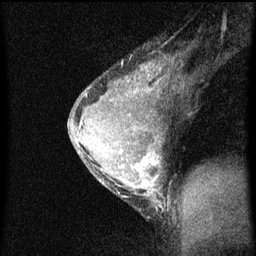
Breast MRI (dynamic contrast-enhanced), one sagittal slice. Slice 42 of 60 in the series (ordered by position). Dynamic contrast-enhanced series, image 2 of 3 at this slice position (ordered by acquisition). 1.5 T. TE 4.2 ms, TR 8 ms. 2 mm slice thickness. 256 × 256 image matrix, field of view 180 × 180 mm. Patient: female, 33 years.
Outlined on this slice (semi-automatic segmentation, software-assisted and operator-edited):
- analysis volume of interest (the breast-tissue region the enhancement analysis was run in; not a lesion): bounding box [x1, y1, x2, y2] px = [68, 58, 181, 211]
- tumour enhancement mask (voxels above the 70 % enhancement threshold inside the analysis volume of interest): [80, 66, 163, 209]